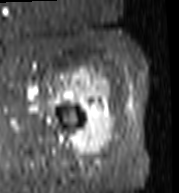
MRI of an extremity soft-tissue mass, one axial slice. Slice 88 of 103 in the series (ordered by position). STIR. MR volume resampled by the dataset authors to the PET/CT grid (not the native acquisition matrix). 3.27 mm slice thickness. 179 × 193 image matrix, field of view 175 × 188 mm. Female patient. From the clinical record (not read from this slice): histological type: undifferentiated – high grade; grade: high; site of the primary tumour: left thigh.
Annotated regions visible in this slice (expert contour drawn on MRI and transferred to this co-registered scan by the dataset authors):
- gross tumour volume including surrounding oedema: box from (x=61, y=69) to (x=115, y=157) px
- gross tumour volume (mass): (x=63, y=69)–(x=115, y=156)